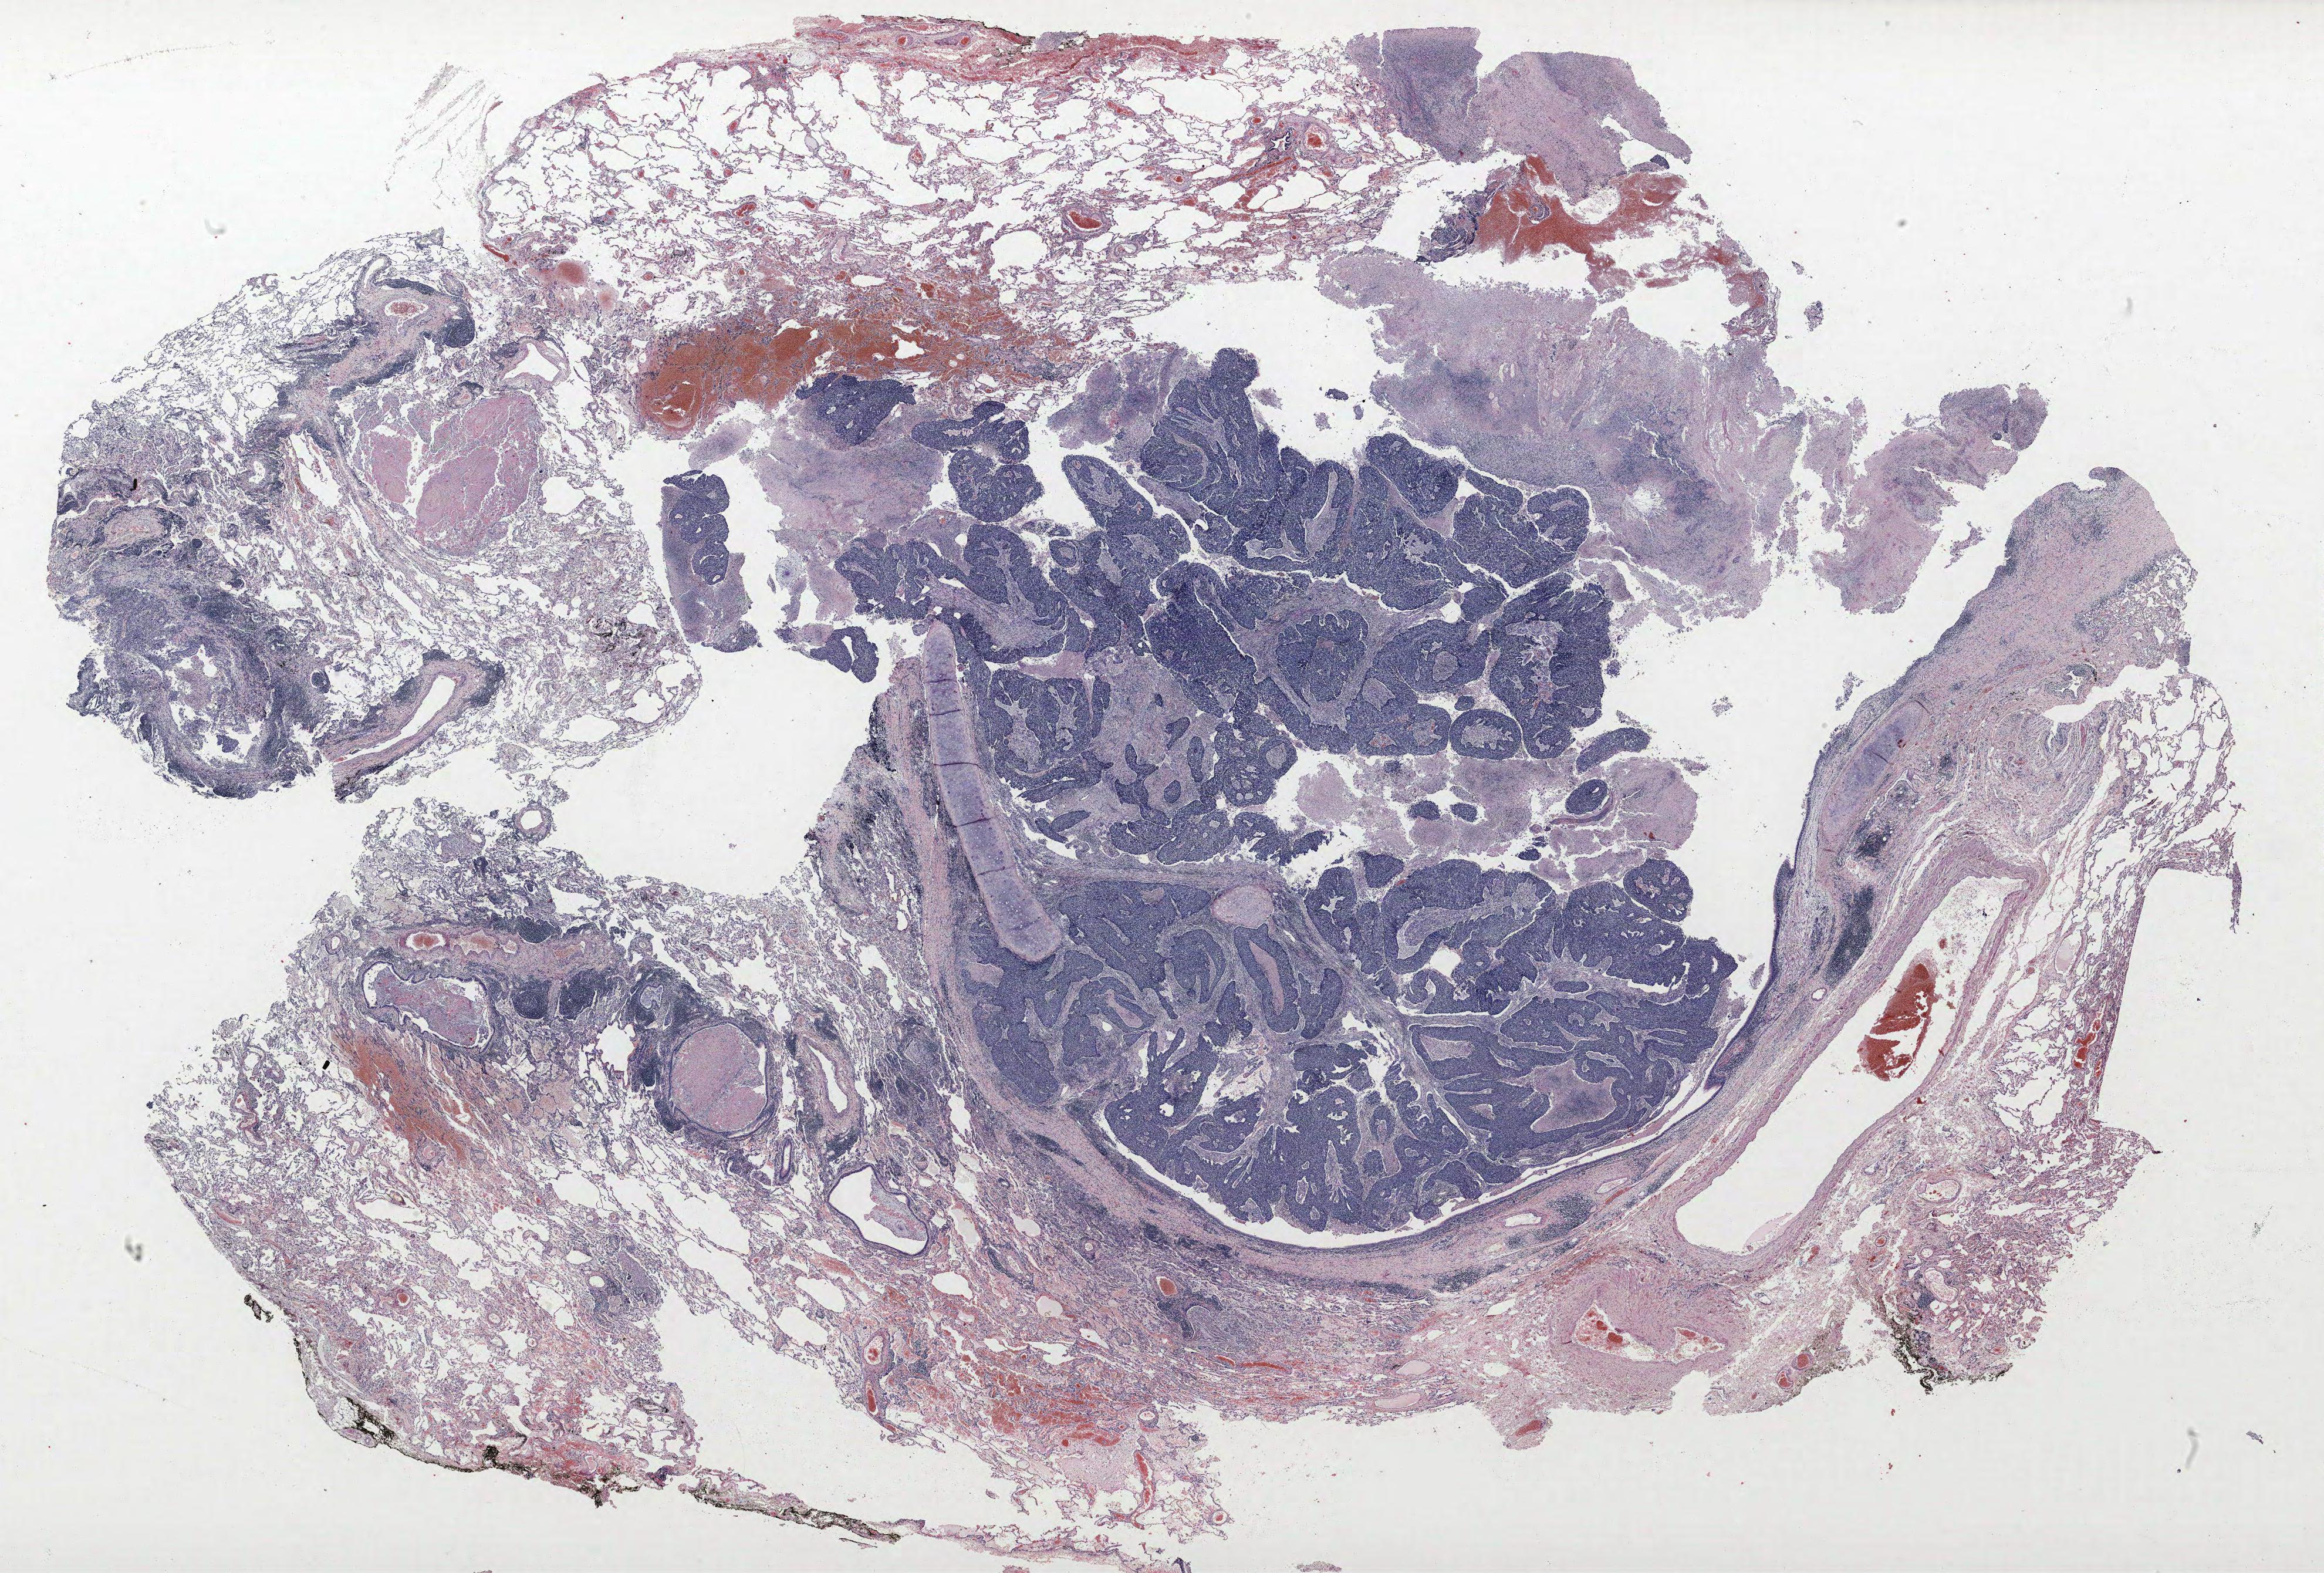
H&E whole-slide image — low-resolution overview of the scanned area, about 31.7 x 21.4 mm (from a 40x scan). Formalin-fixed paraffin-embedded (FFPE) section. Lung. Male patient, aged 66 at enrolment. Current smoker at enrolment.
Stage (AJCC 6th edition): IA. ICD-O-3 topography: upper lobe of lung (C34.1). Tumour size (pathology): 23 mm. Participant's lung-cancer diagnosis: Squamous cell carcinoma, NOS (ICD-O-3 8070/3). Primary tumour location (clinical record): left upper lobe. Note: participant had 2 primary lung cancers recorded; fields above describe the first.